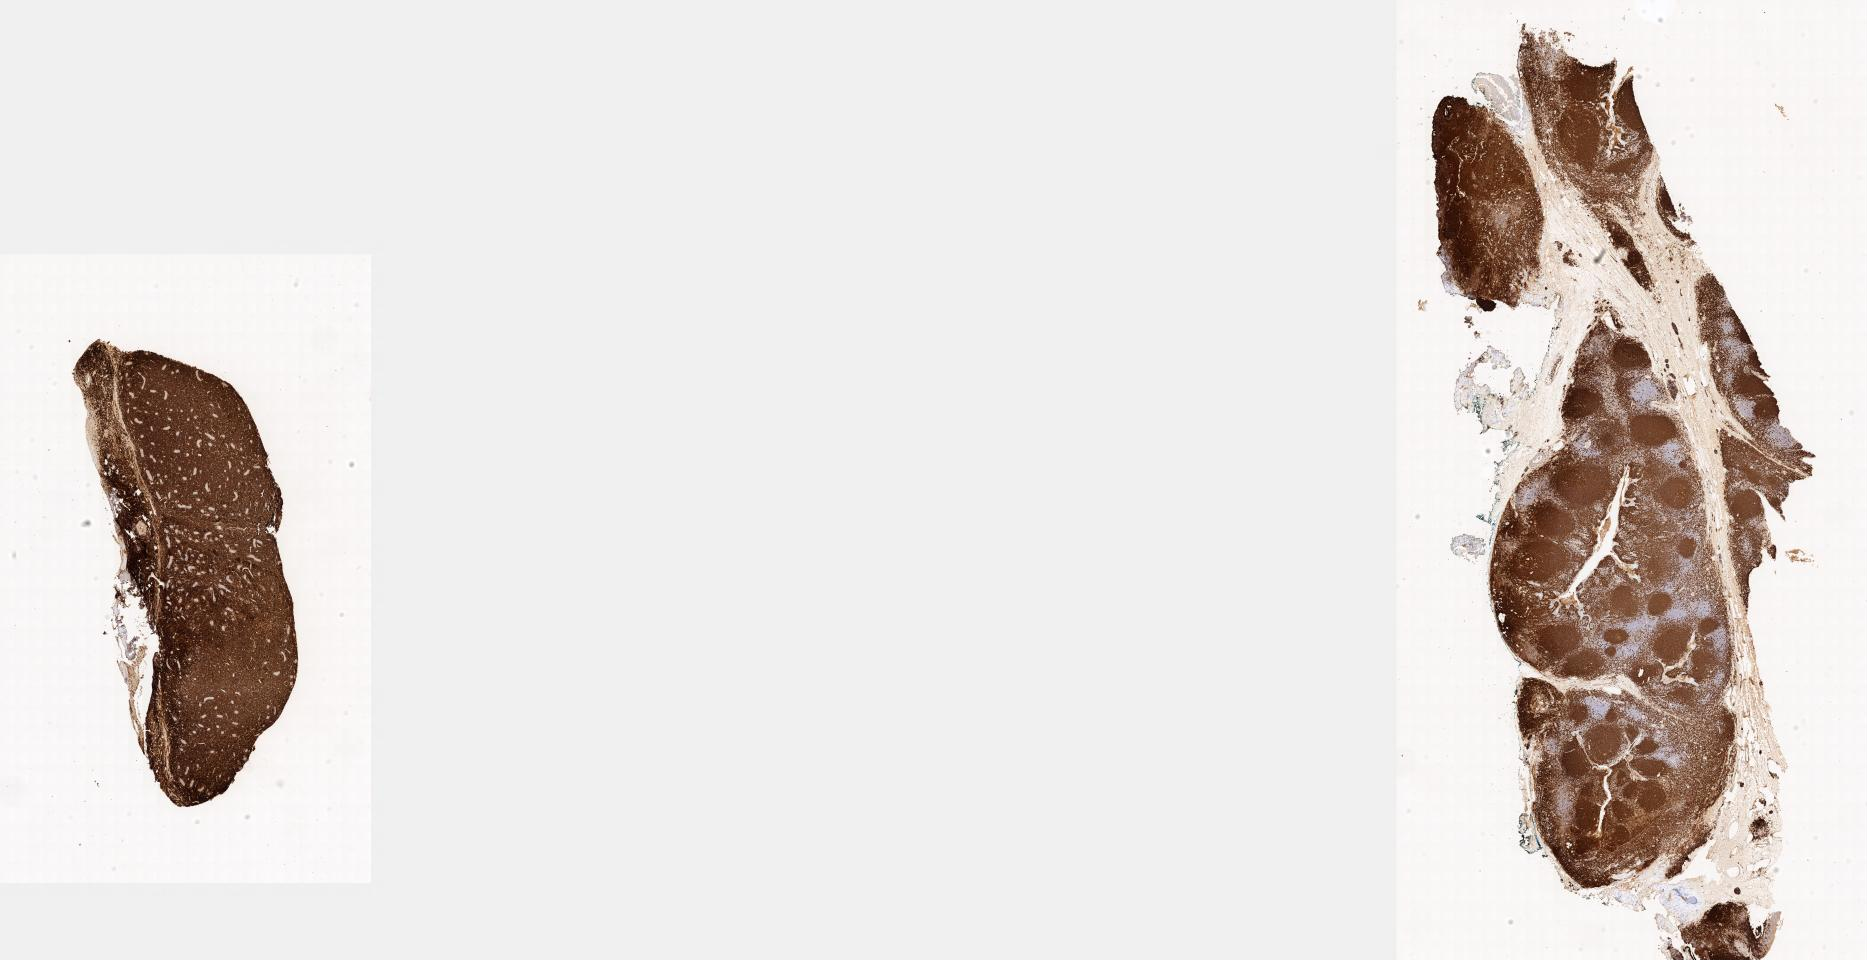
Whole-slide image, immunohistochemical stain for CD20, shown as a low-resolution overview of the whole scanned area. Tumor tissue. Anatomic site: testis. Patient: male, age at initial diagnosis 8 years.
- histologic diagnosis: Burkitt lymphoma, NOS